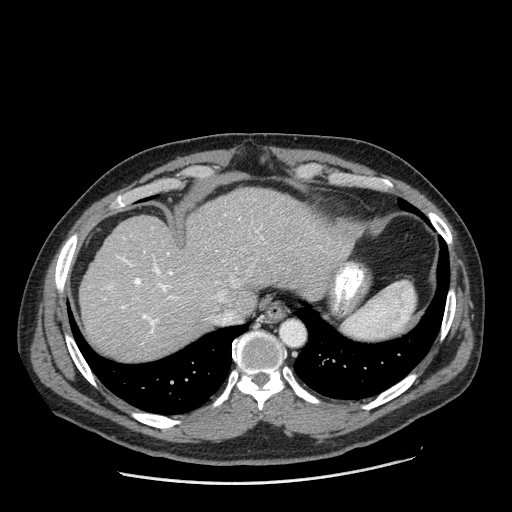
Contrast-enhanced abdominal CT (liver protocol), one axial slice. Position 157 of 198 along the scan axis. Reconstruction kernel STANDARD. 120 kVp. One of 2 acquisitions stored at this slice position. Soft-tissue window (W 400 / L 40 HU). 512 × 512 image matrix, field of view 400 × 400 mm. From the clinical record (not read from this slice): diagnosis: hepatocellular carcinoma (patient treated with transarterial chemoembolisation; whether this scan precedes or follows treatment is not stated here); TNM stage (as recorded): Stage-II; Child-Pugh class: A; tumour differentiation: moderately differentiated.
Outlined on this slice (semi-automatically segmented with operator editing):
- abdominal aorta: bounding box [x1, y1, x2, y2] px = [282, 322, 303, 344]
- liver parenchyma outside the tumour (the mass and vessels are separate outlines, so this box may not span the whole liver): [80, 188, 359, 360]
- liver vessels: [107, 217, 263, 333]